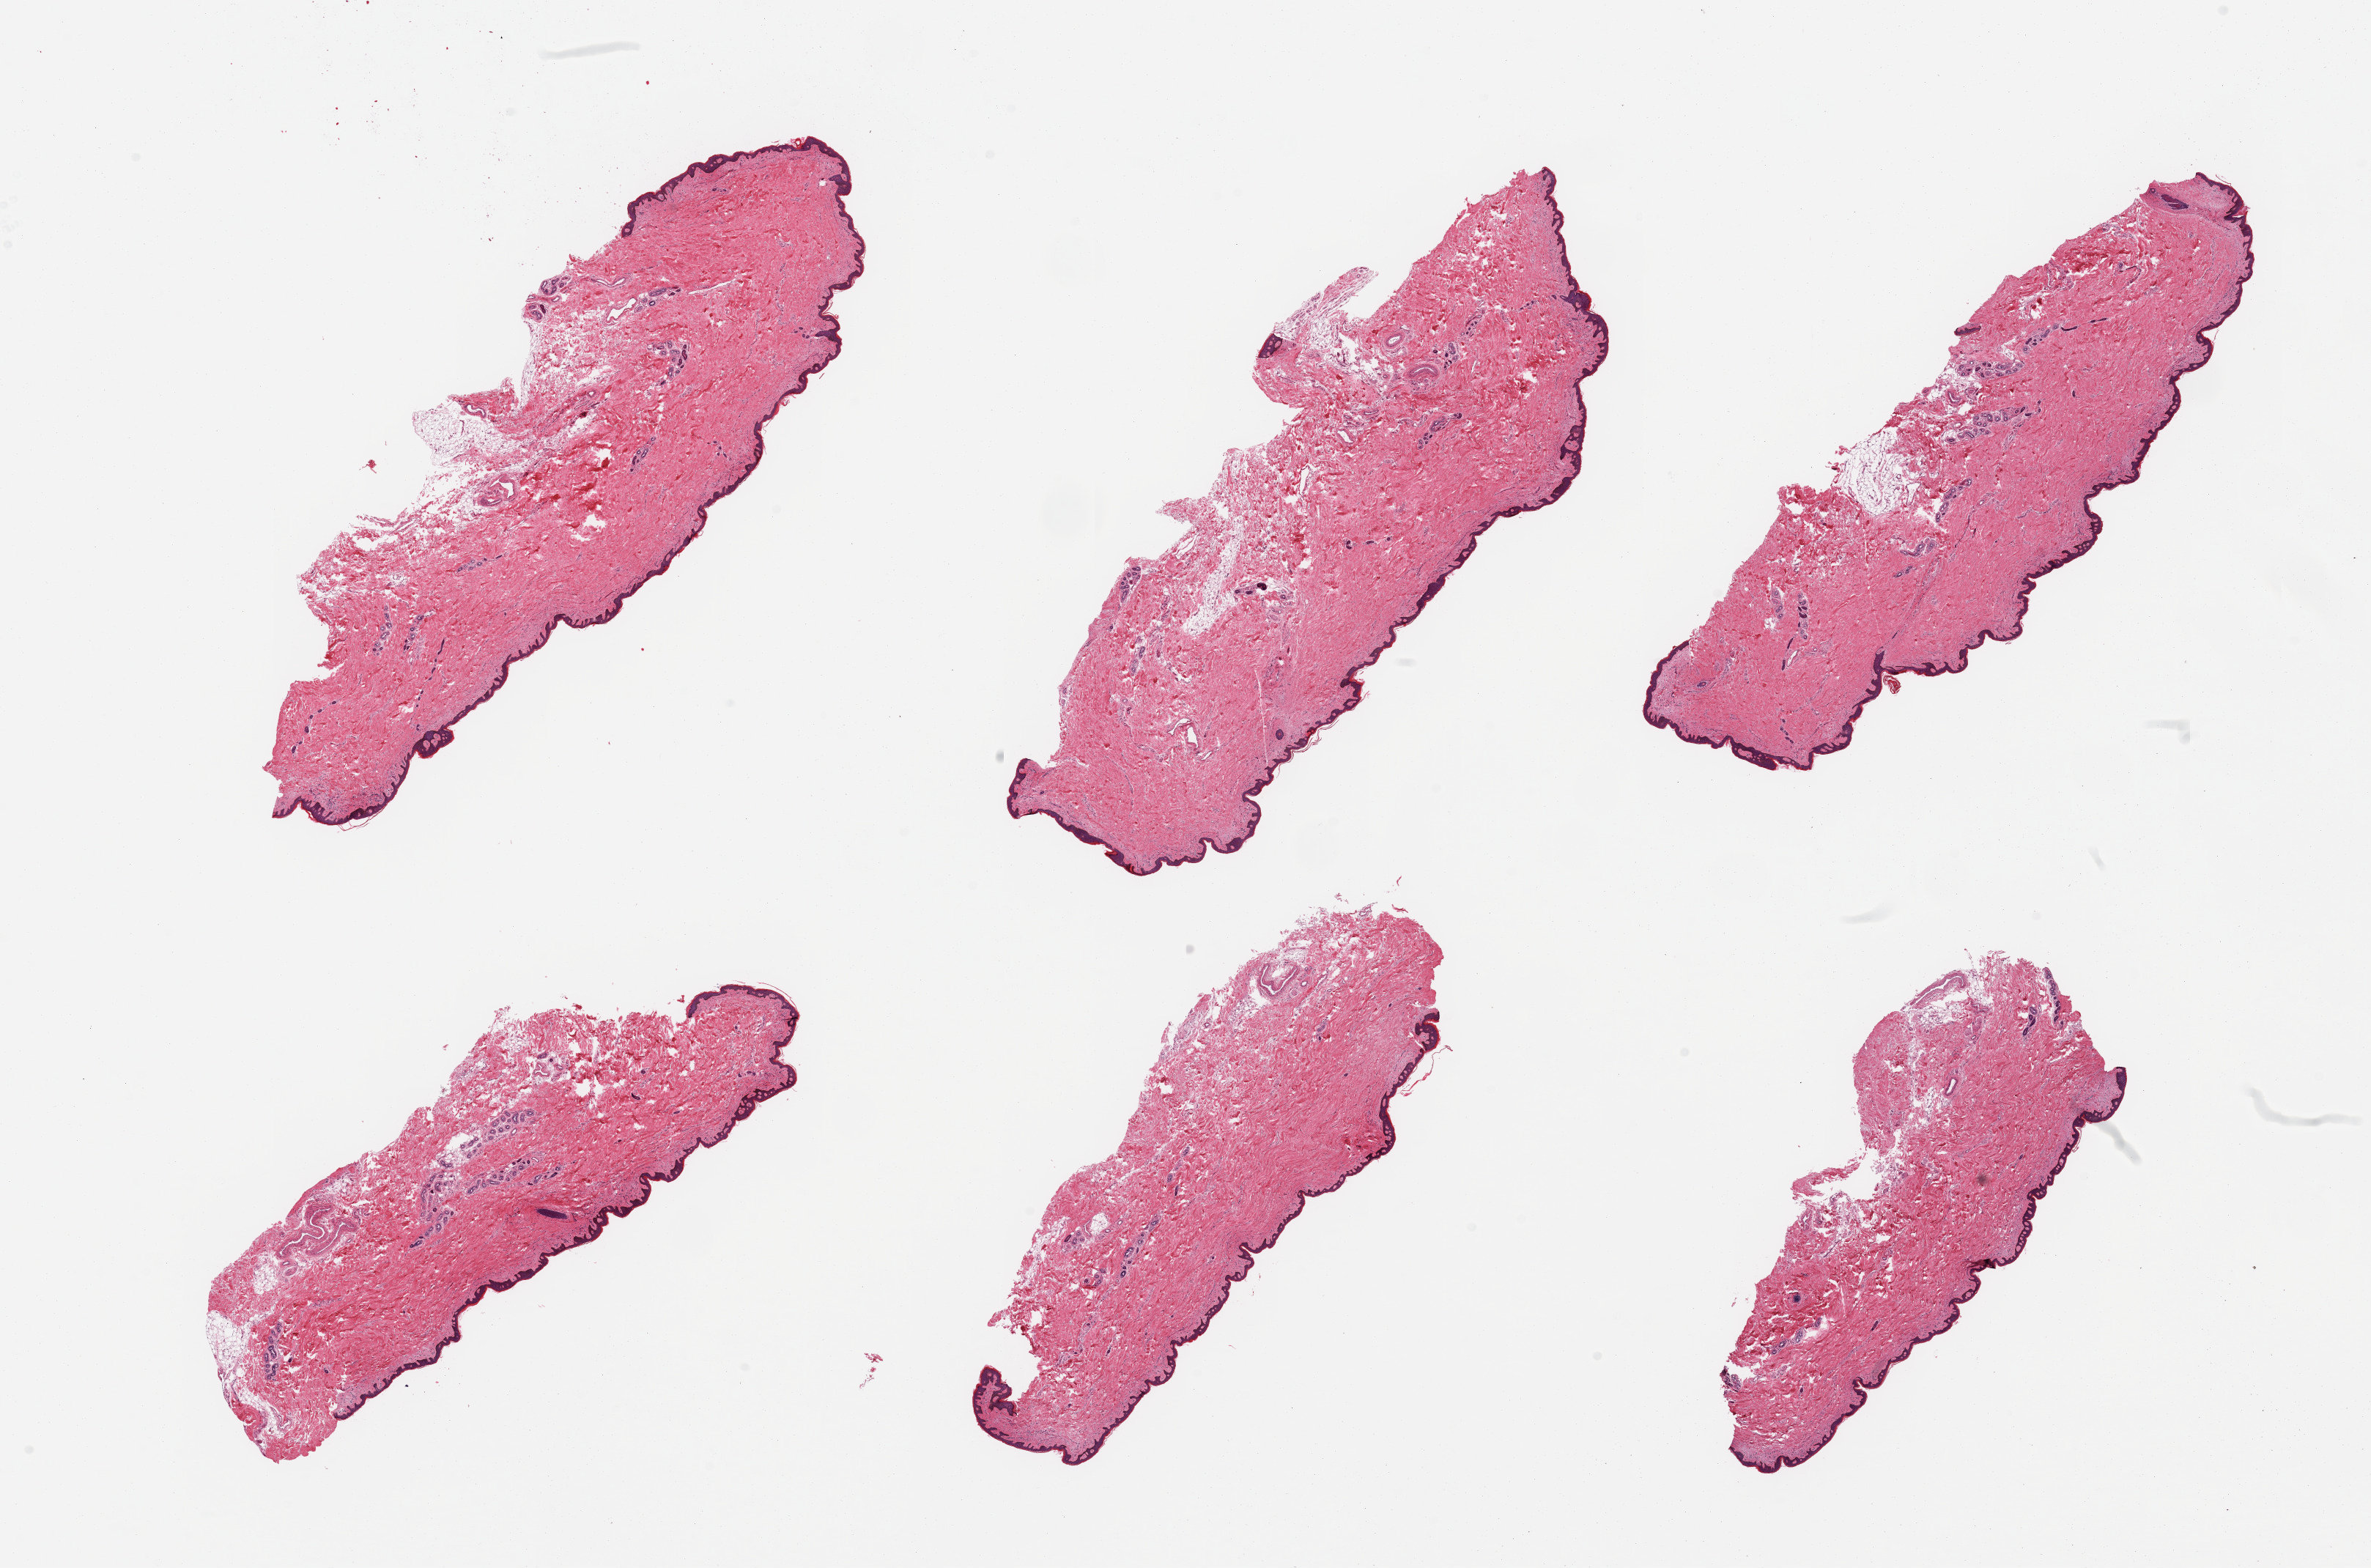
Whole-slide image, H&E stain, whole scanned area (about 25.6 x 16.9 mm) shown as a low-resolution overview, PAXgene-fixed, paraffin-embedded tissue, section of skin of suprapubic region (target tissue), donor tissue sample.
Pathologist's review note for this sample: 6 pieces; ~5% external/internal (periadnexal) fat.